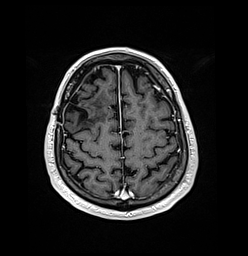
Brain MRI from a brain-tumour surgery series, one axial slice; slice 40 of 176 in the series (ordered by position); T1-weighted post-contrast; 248 × 256 image matrix, field of view 242 × 250 mm. From the clinical record (not read from this slice): histopathology: Oligodendroglioma; WHO grade: 3; IDH mutation: yes.
Outlined on this slice (expert manual segmentation):
- previous resection cavity: bounding box [x1, y1, x2, y2] px = [66, 92, 89, 125]